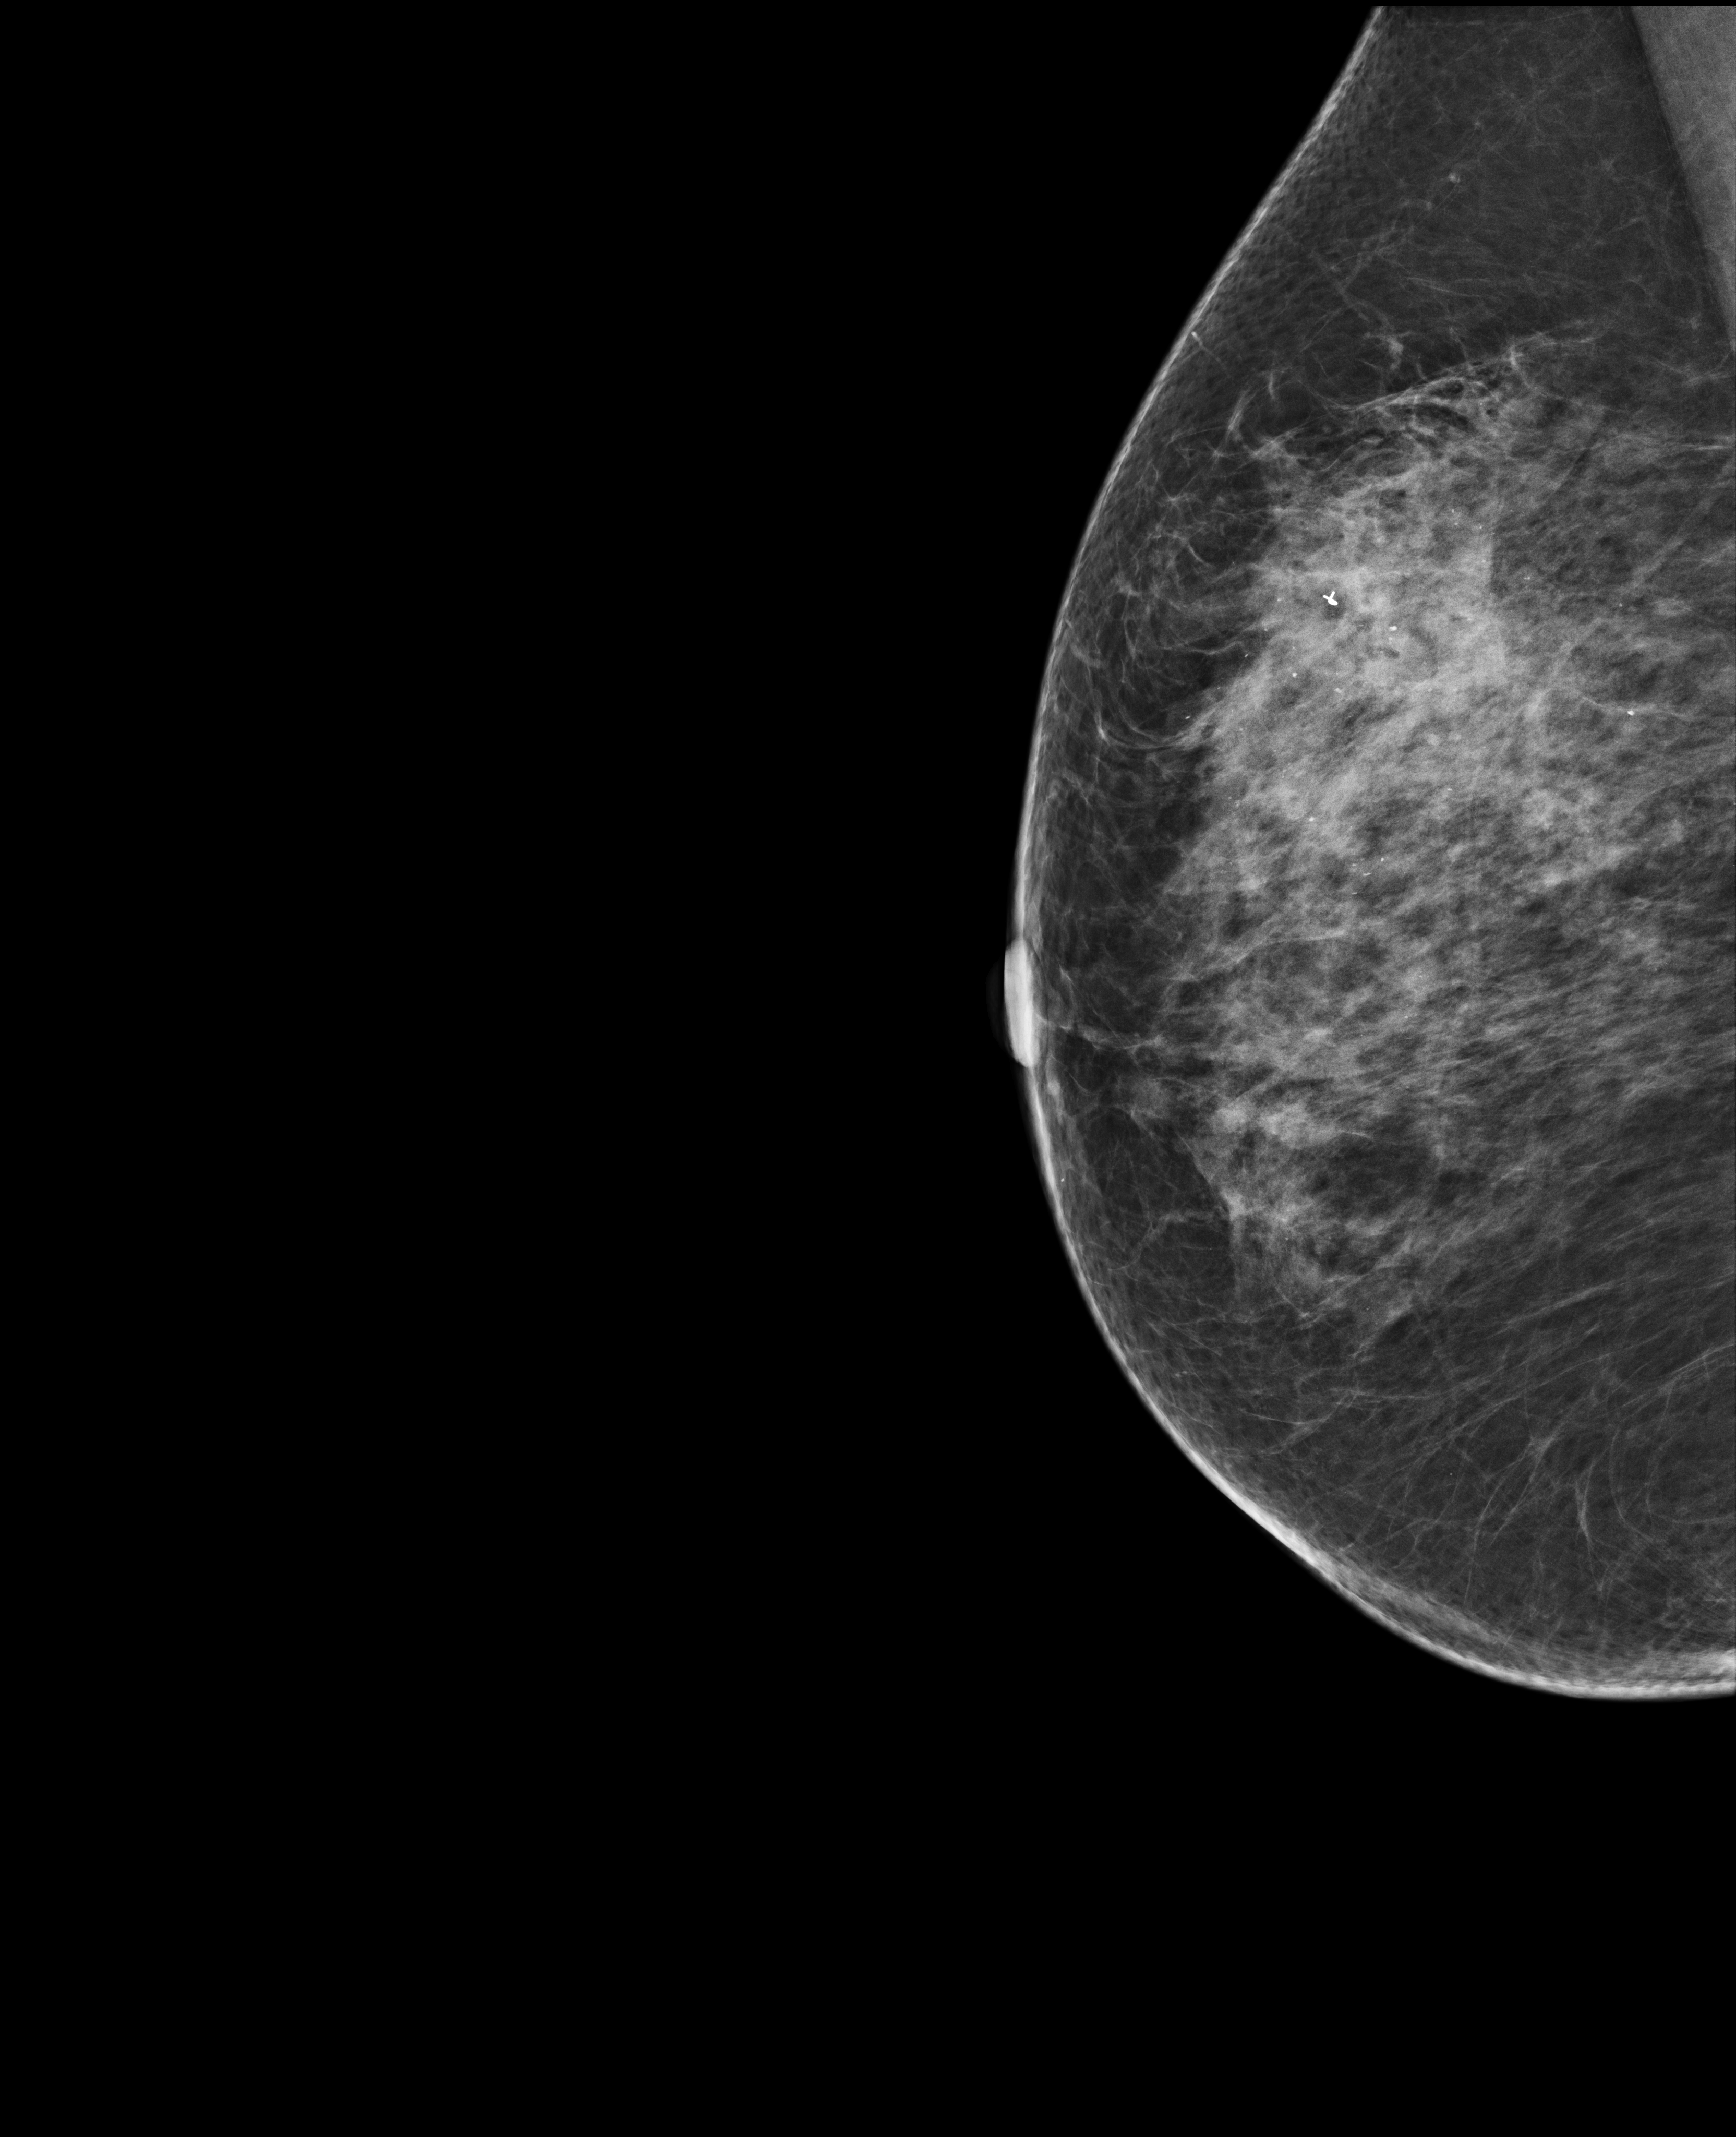
Diagnostic examination (additional views), compressed breast thickness 64 mm. Female patient, age 71 years.
Image type: full-field digital mammogram. Breast: right. Projection: MLO view.